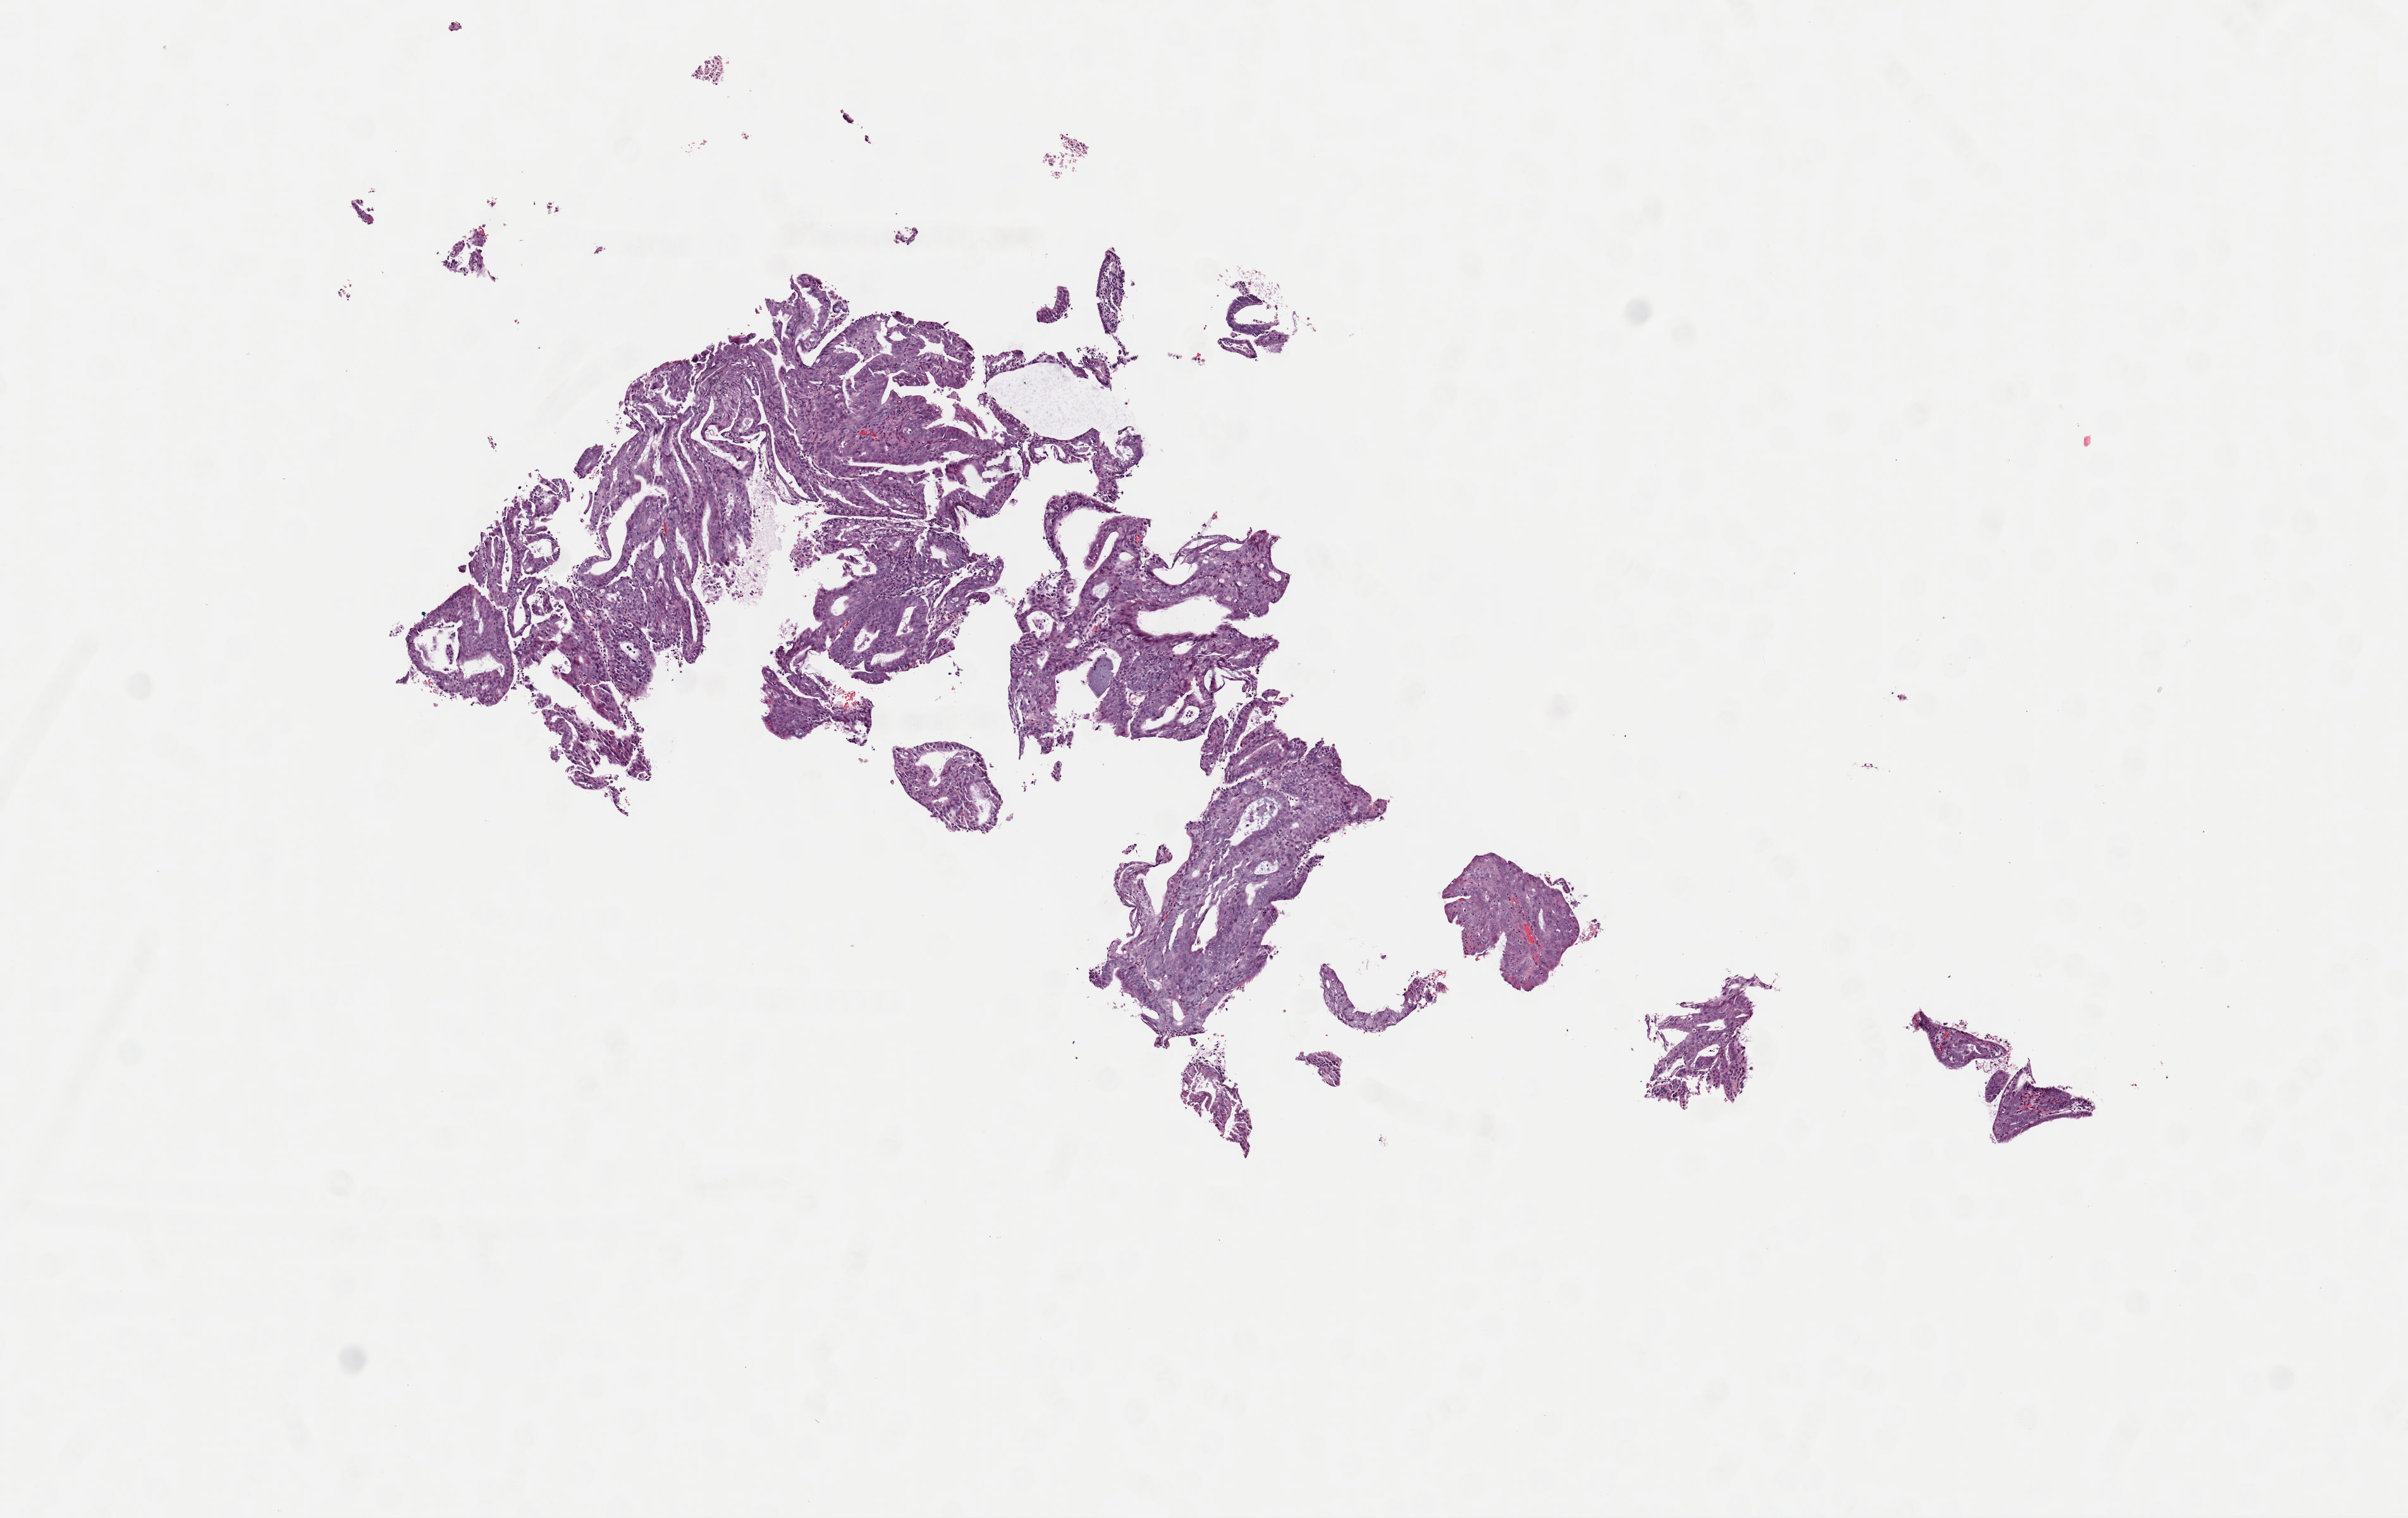
H&E whole-slide image, shown as a low-resolution overview of the whole scanned area (about 7.5 x 4.7 mm, from a 40x scan); frozen section from the bottom of the tissue portion; primary tumour sample from the uterus. Patient: female, age at initial diagnosis 61 years. Histologic grade: G3 (poorly differentiated). Composition of this section per pathologist review: tumour cells 99%, tumour nuclei 80%, normal cells 0%, stromal cells 0%, necrosis 1%. Inflammatory infiltration, as recorded: lymphocyte infiltration 1%, monocyte infiltration 0%, neutrophil infiltration 0%.
FIGO stage: IIIC. Pathologic diagnosis: Serous cystadenocarcinoma, NOS.